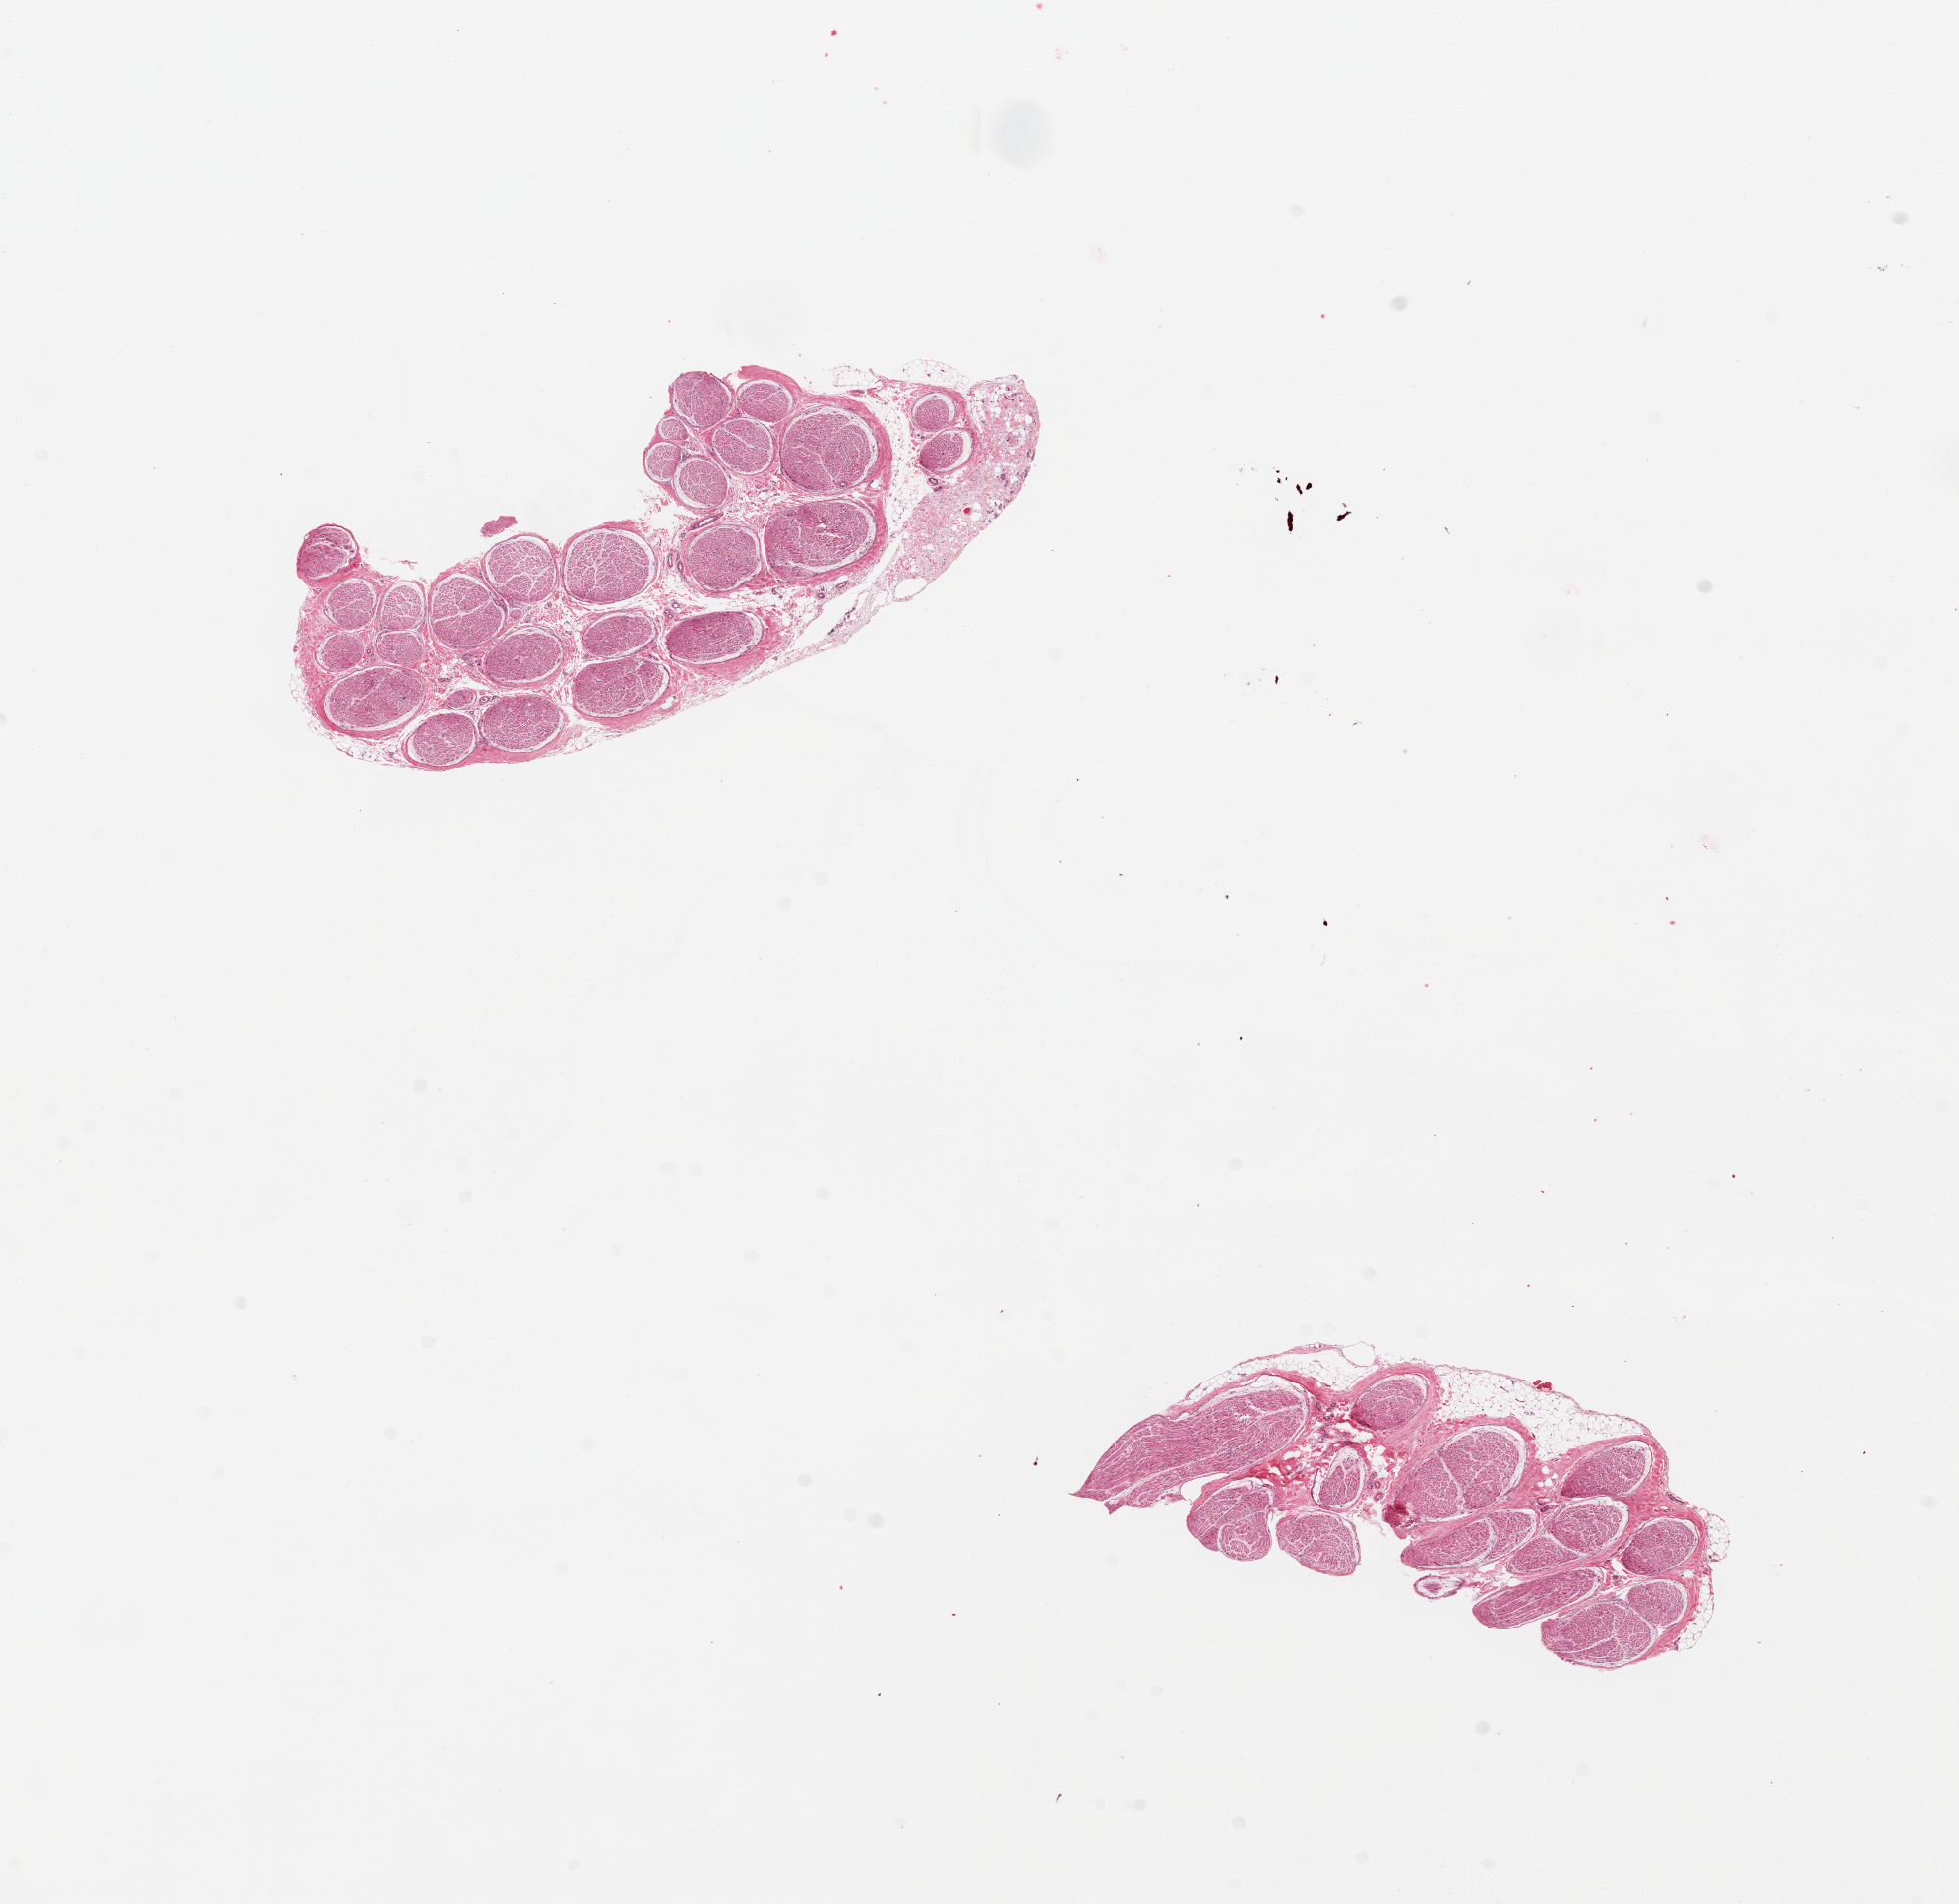
Whole-slide image, H&E stain, brightfield, low-resolution overview of the scanned area, about 15.8 x 15.3 mm (acquisition: 20x scan); PAXgene-fixed paraffin-embedded (PFPE) section; sampled site (target tissue): tibial nerve; tissue donor sample. Donor: female.
Reviewer comment on this tissue sample: 2 pieces; ~10% attached fat/fibroadipose tissue.